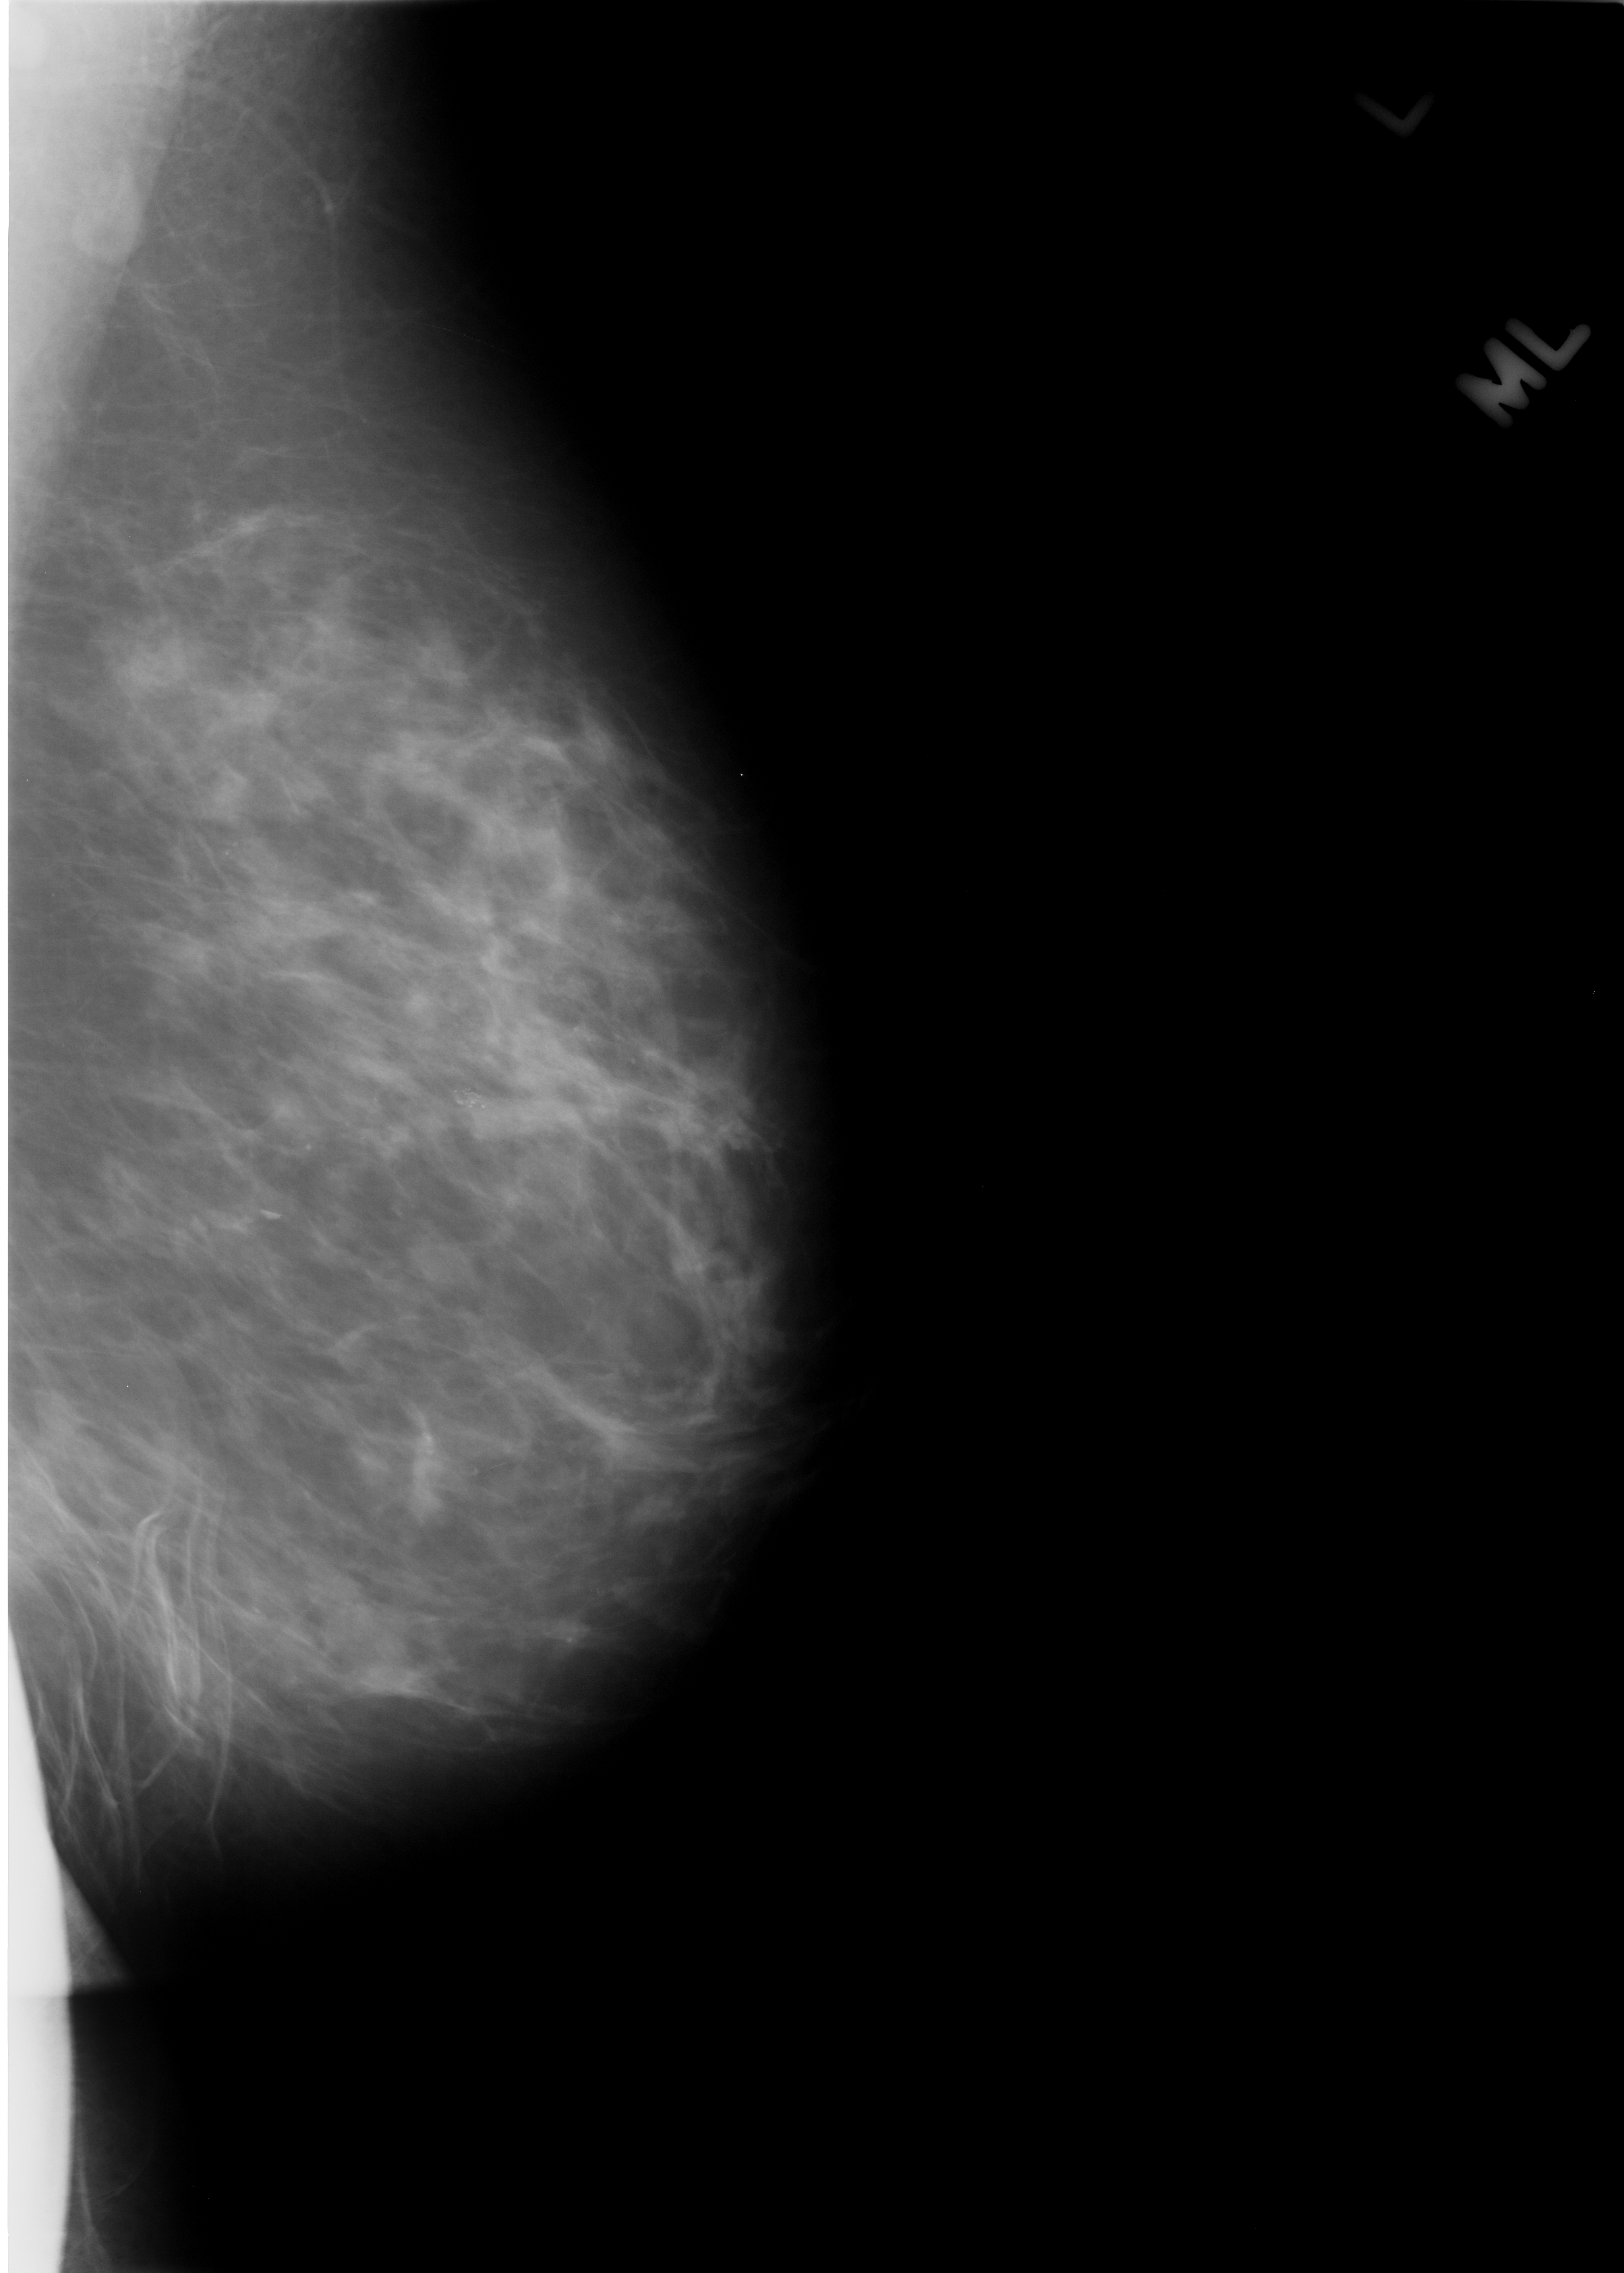
Digitized screen-film mammogram; left breast; MLO view; BI-RADS breast density category 2 (scale 1–4); 1624 × 2273 image matrix.
Marked abnormalities (boxes around the expert regions of interest):
- calcifications, morphology pleomorphic, distribution clustered; BI-RADS assessment category 4; pathology result (as recorded, not read from the image): benign: bounding box [x1, y1, x2, y2] px = [390, 1042, 516, 1149]